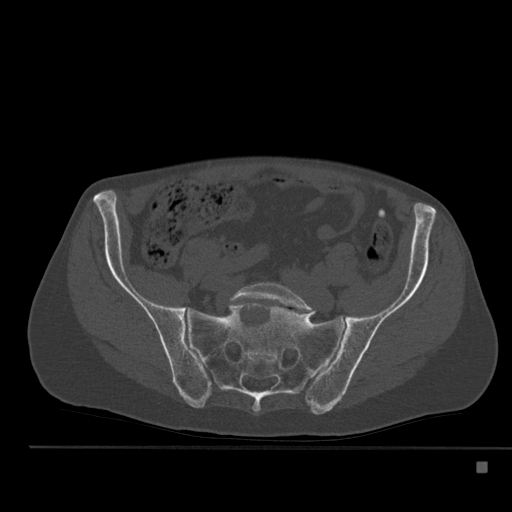
CT including the spine, one axial slice; slice 102 of 517 in the series (ordered by position); 120 kVp; bone window (W 1800 / L 400 HU); 512 × 512 image matrix, field of view 408 × 408 mm. Male patient, age 70 years. Case-level facts recorded for this patient, not image findings: primary cancer: renal.
Structures marked on this image (semi-automatic segmentation, software-assisted and operator-edited):
- L5 vertebra: bounding box (x1, y1, x2, y2) in pixels: (230, 282, 315, 314)